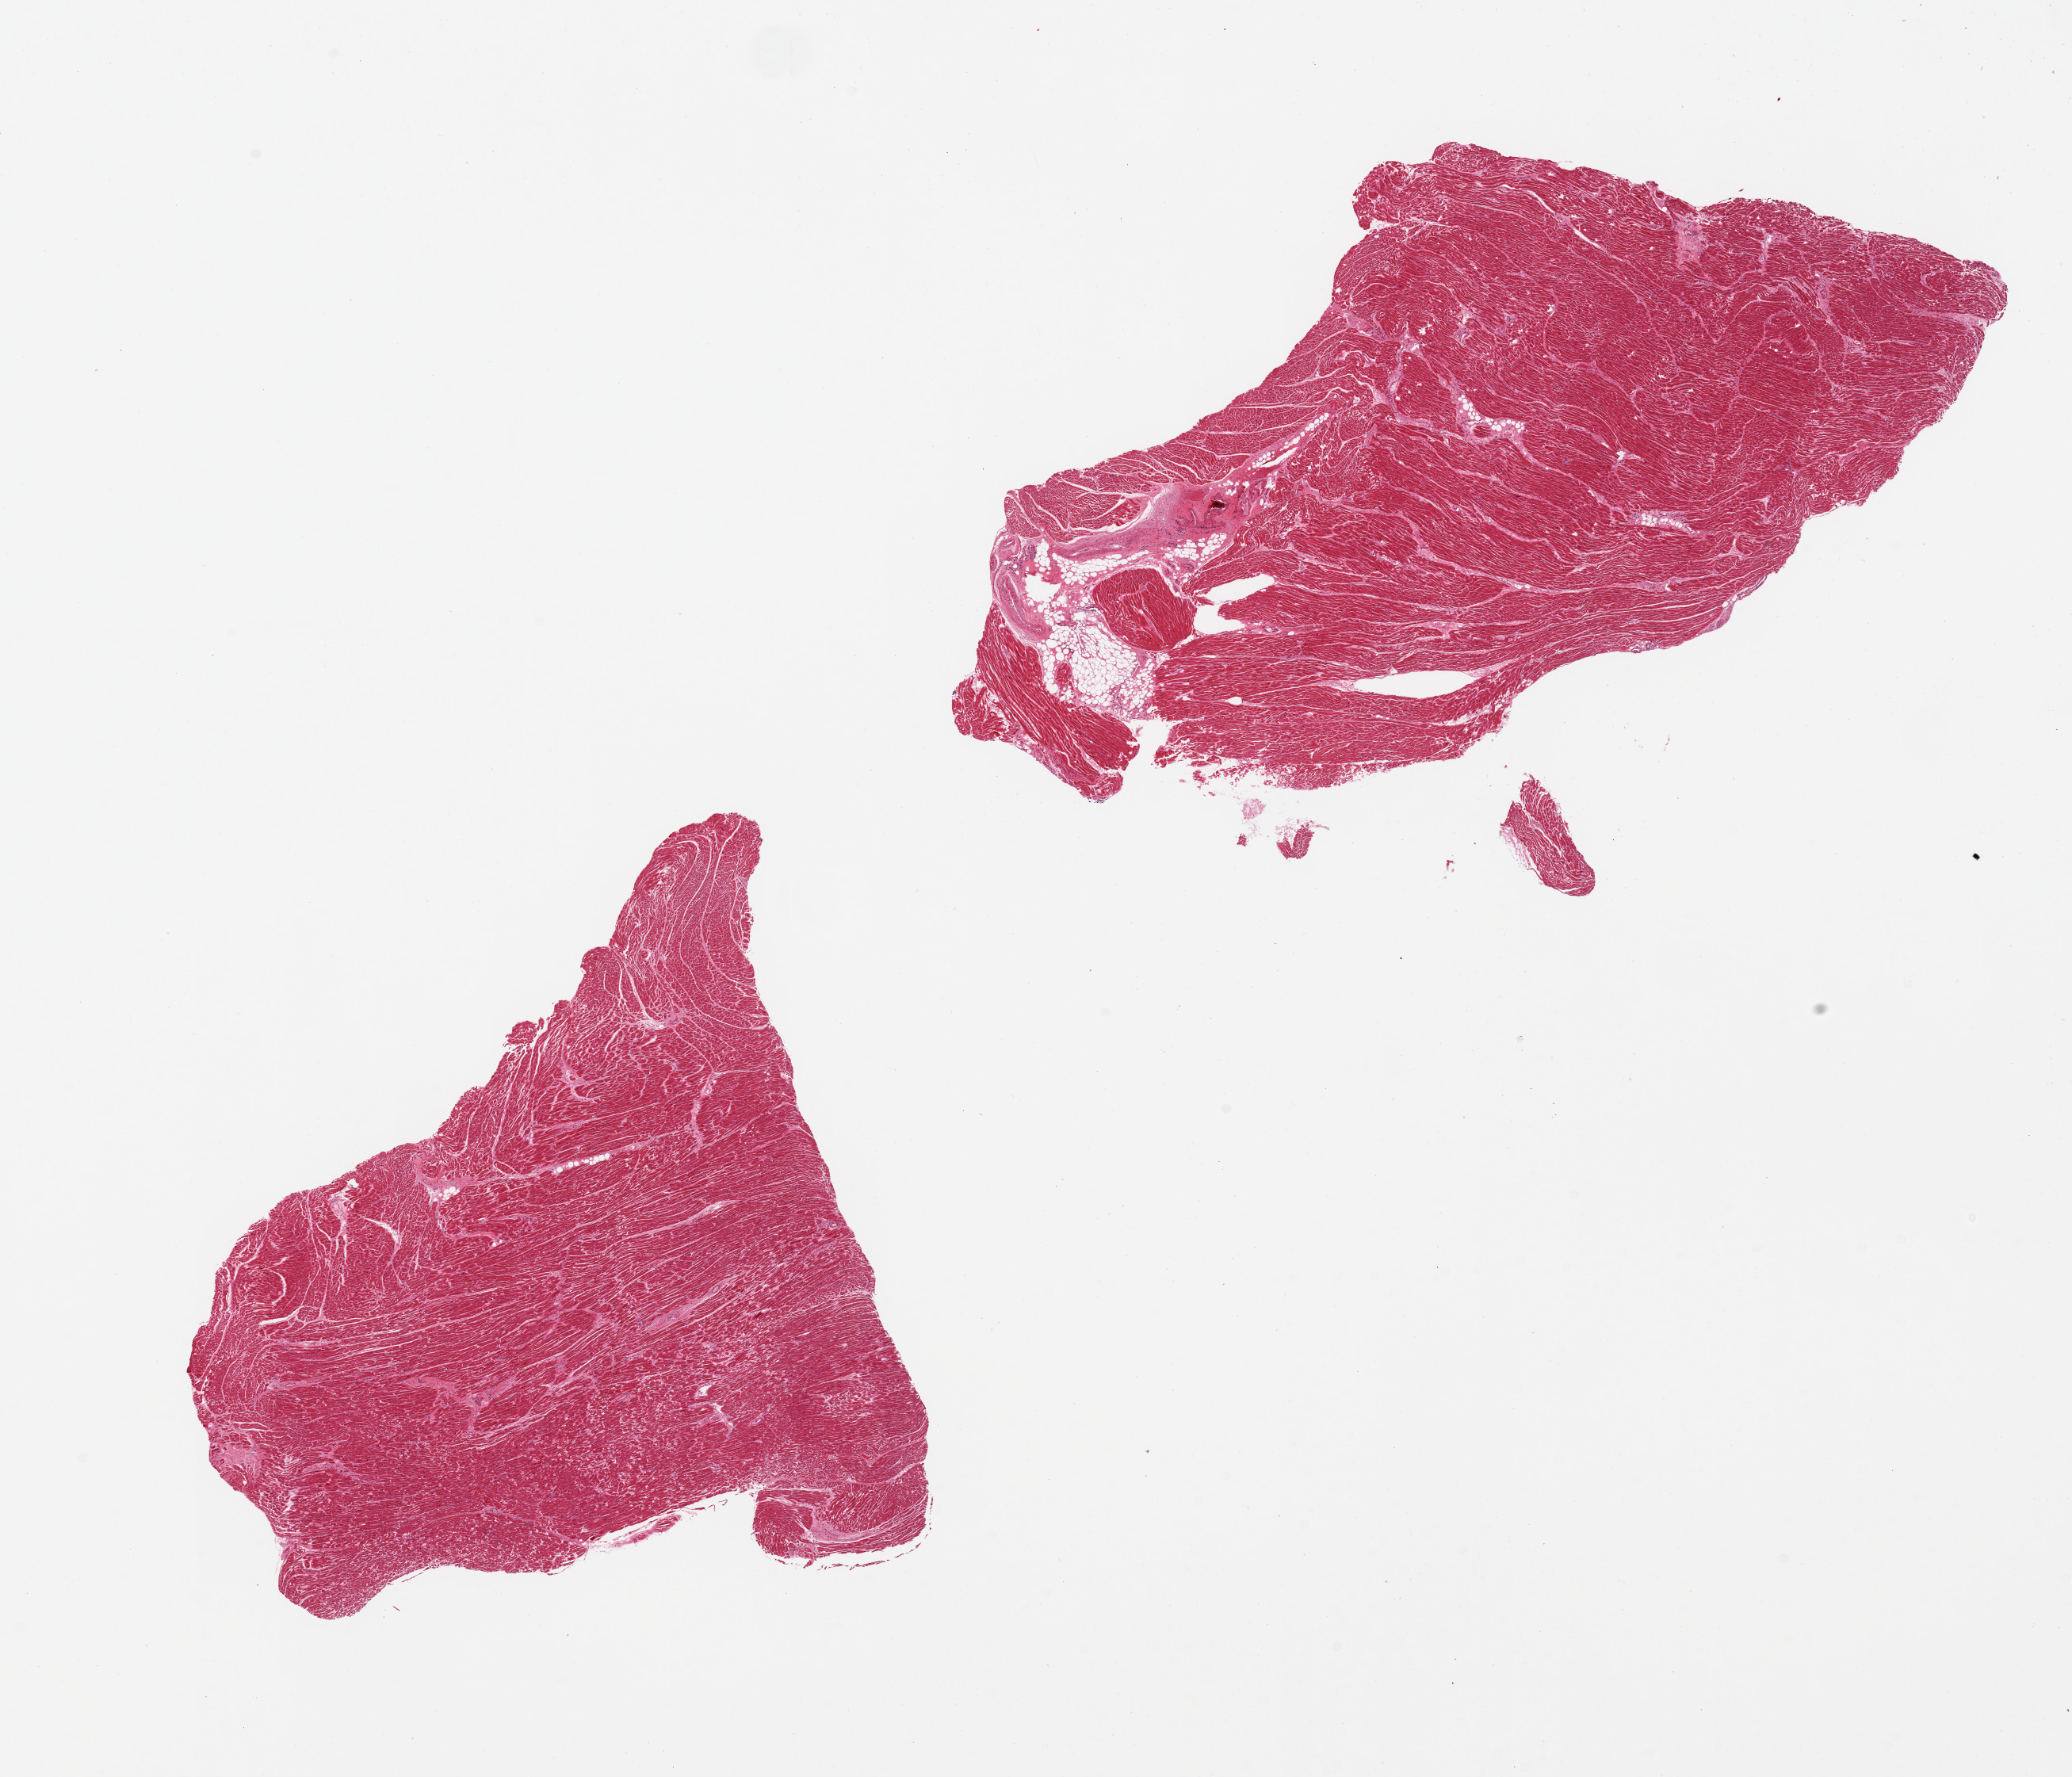
Whole-slide image, haematoxylin and eosin stain, brightfield — low-resolution overview of the scanned area, about 20.7 x 17.7 mm (acquisition: 20x scan). PAXgene-fixed paraffin-embedded (PFPE) section. Section of heart (target tissue). Donor tissue sample. Male donor.
• pathologist's review note for this sample: 2 pieces; mild interstitial fibrosis; larger piece shows 10% of internal fat